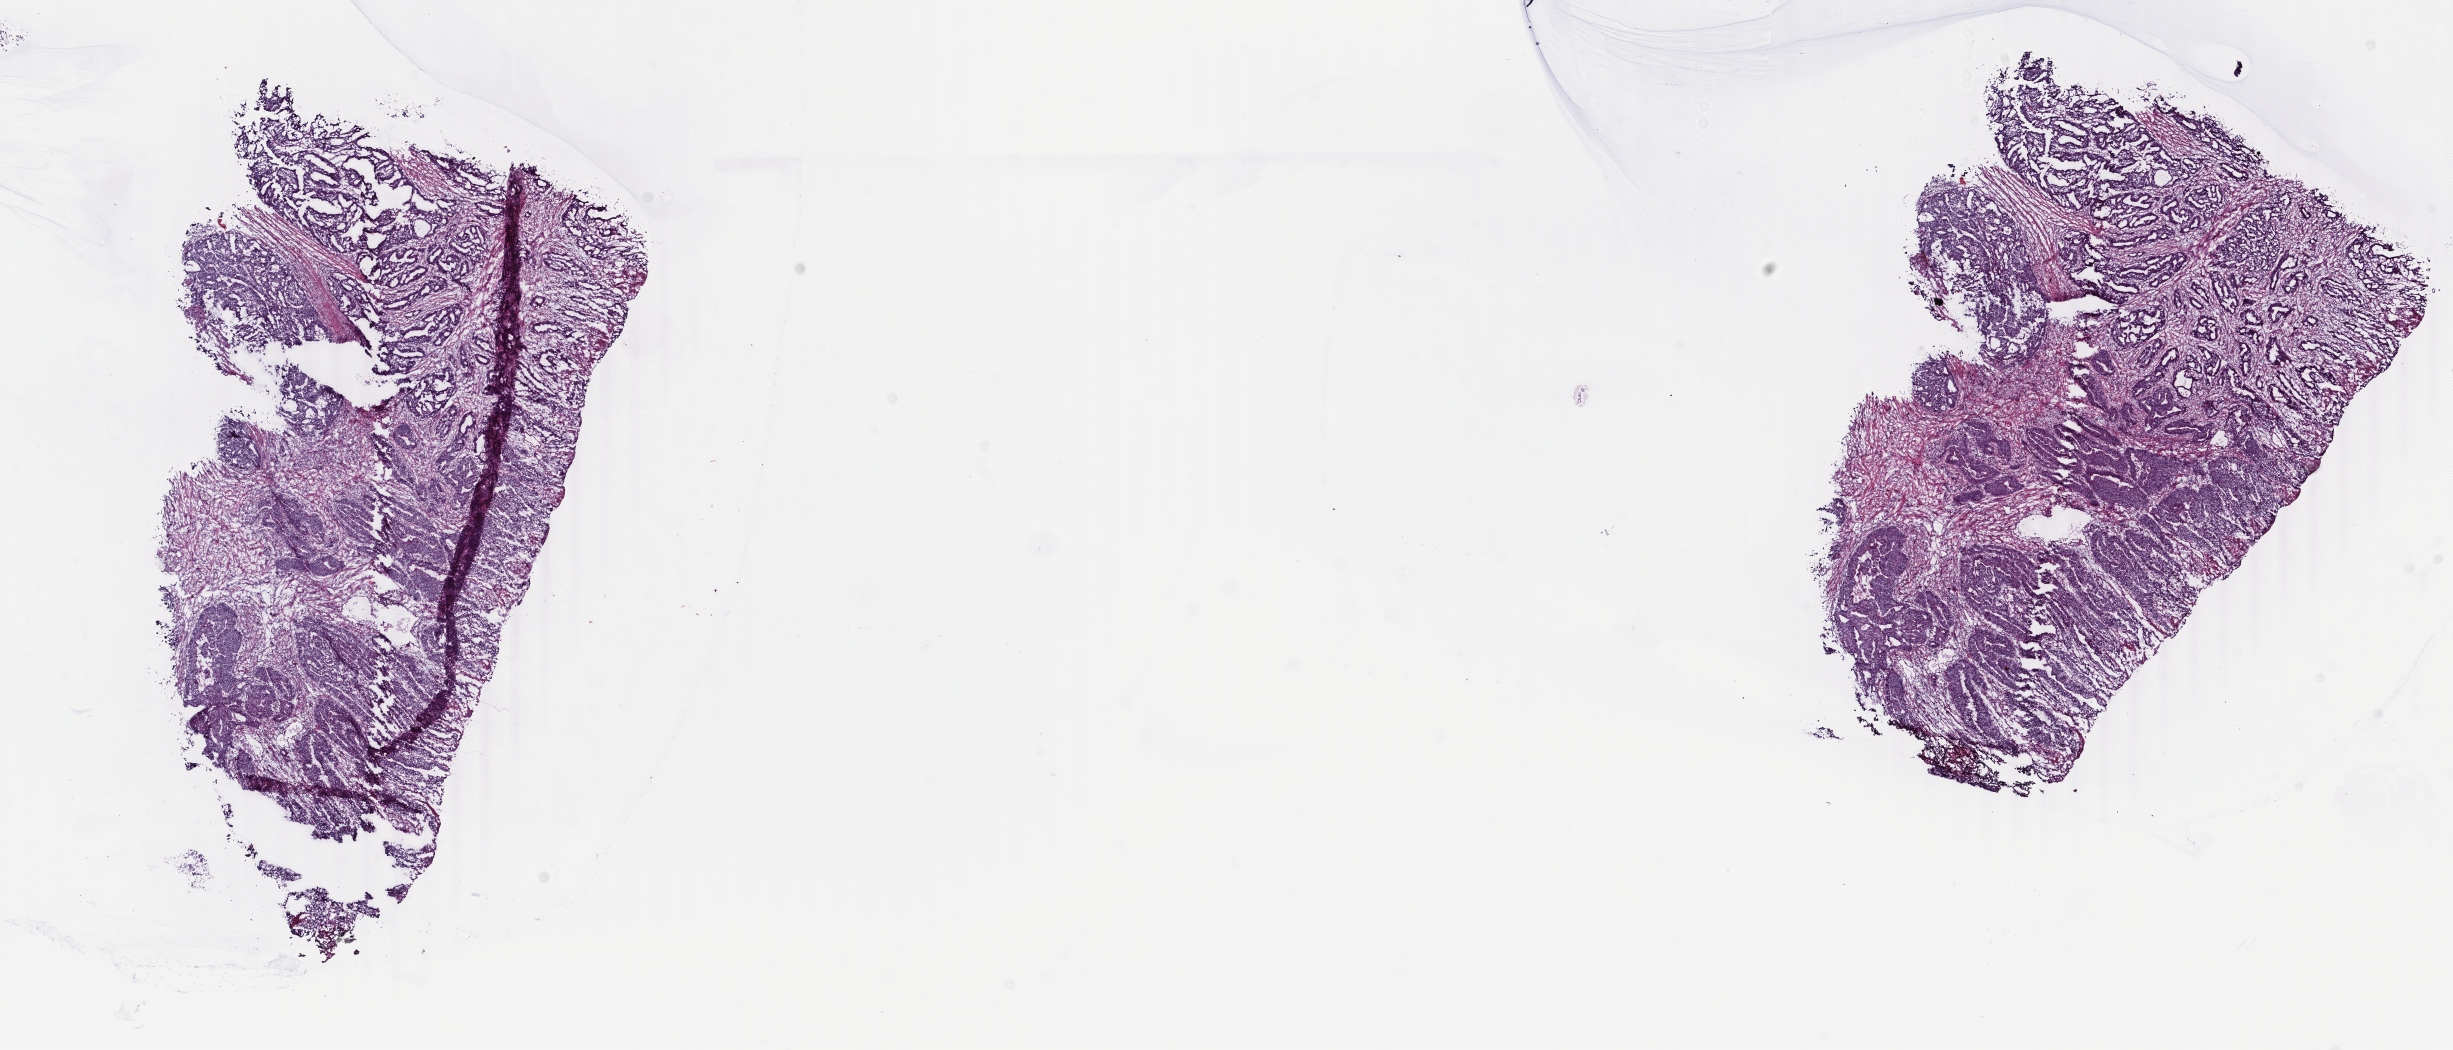
Digitized Hematoxylin and eosin (H&E) stained tissue section (whole slide) — low-resolution overview of the scanned area, about 19.5 x 8.4 mm (acquisition: 40x scan). Frozen section. Rectum, primary tumour sample. Patient: male, age at initial diagnosis 71 years. Pathologist review of this section (percent, as recorded): tumour cells 80%, tumour nuclei 85%, normal cells 0%, stromal cells 18%, necrosis 2%. Inflammatory infiltration, as recorded: lymphocyte infiltration 7%, monocyte infiltration 1%, neutrophil infiltration 2%.
- lymph nodes positive (case pathology): 18 of 30 examined
- diagnosis: Adenocarcinoma, NOS
- AJCC pathologic stage: III (5th edition)